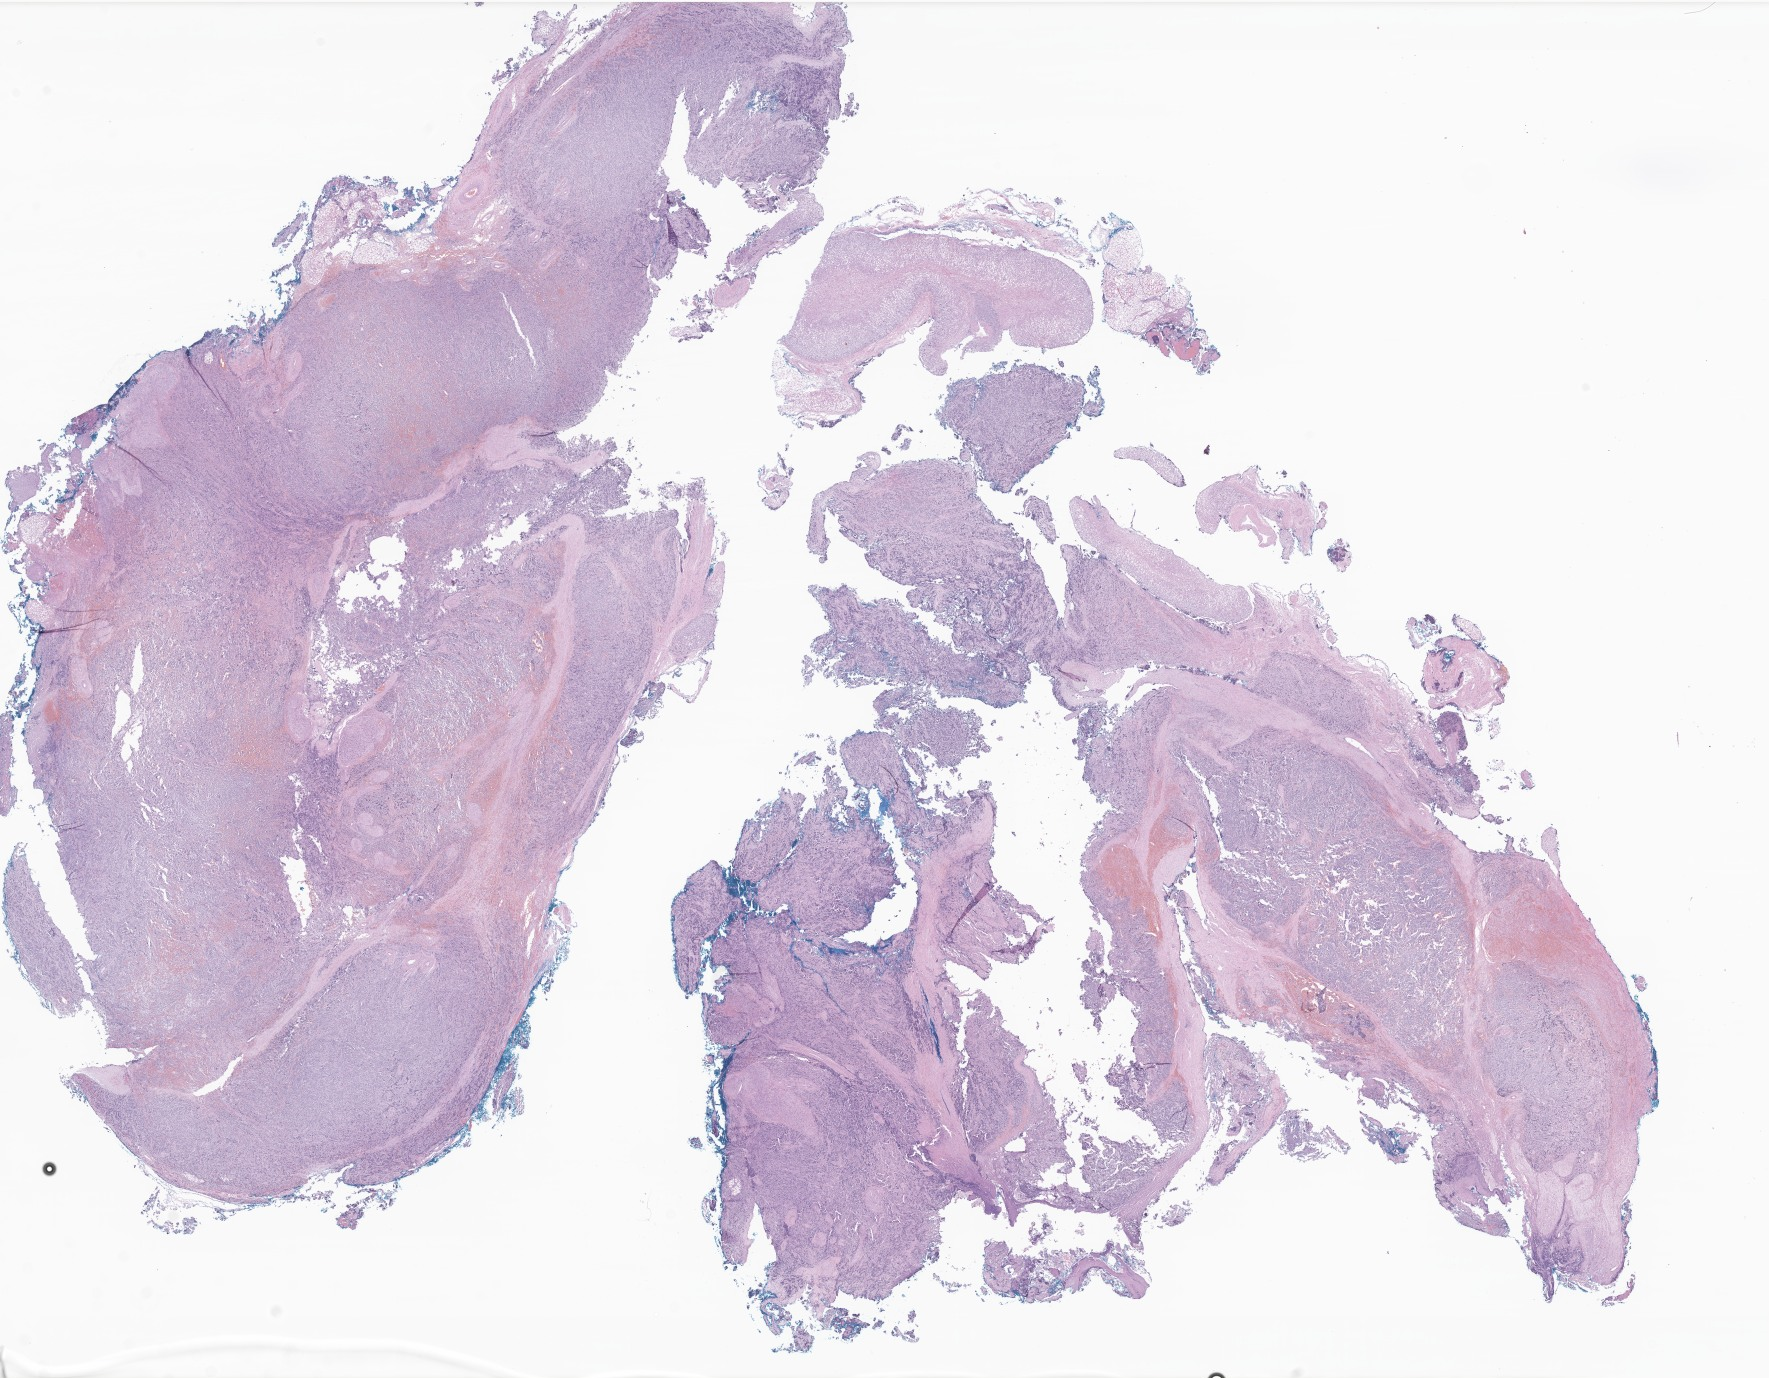
Whole-slide image, haematoxylin and eosin stain of tumor tissue from the adrenal gland — shown as a low-resolution overview of the whole scanned area (about 29.8 x 23.2 mm); formalin-fixed, paraffin-embedded (FFPE) tissue. Female patient, age 113 days.
Diagnosis: Neuroblastoma, NOS.